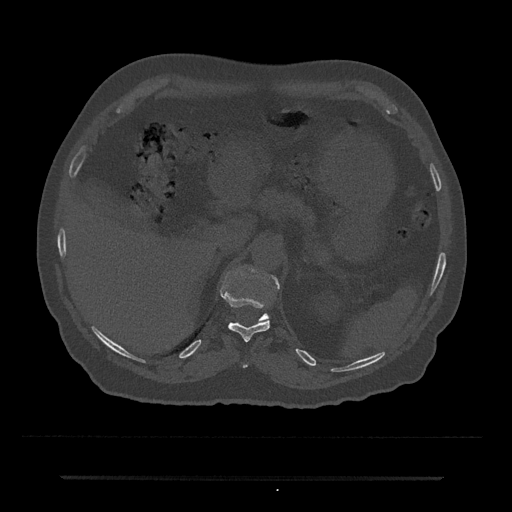
CT including the spine, one axial slice. Position 171 of 797 along the scan axis. 120 kVp. Bone window (W 1800 / L 400 HU). 0.5 mm slice thickness. 512 × 512 image matrix, field of view 437 × 437 mm. Male patient, age 69 years. Case-level facts recorded for this patient, not image findings: primary cancer: prostate.
Outlined on this slice (semi-automatic segmentation, software-assisted and operator-edited):
- T10 vertebra: bounding box <242,363,248,368> (left, top, right, bottom; pixels)
- T11 vertebra: <222,292,270,342>
- T12 vertebra: <259,275,280,321>